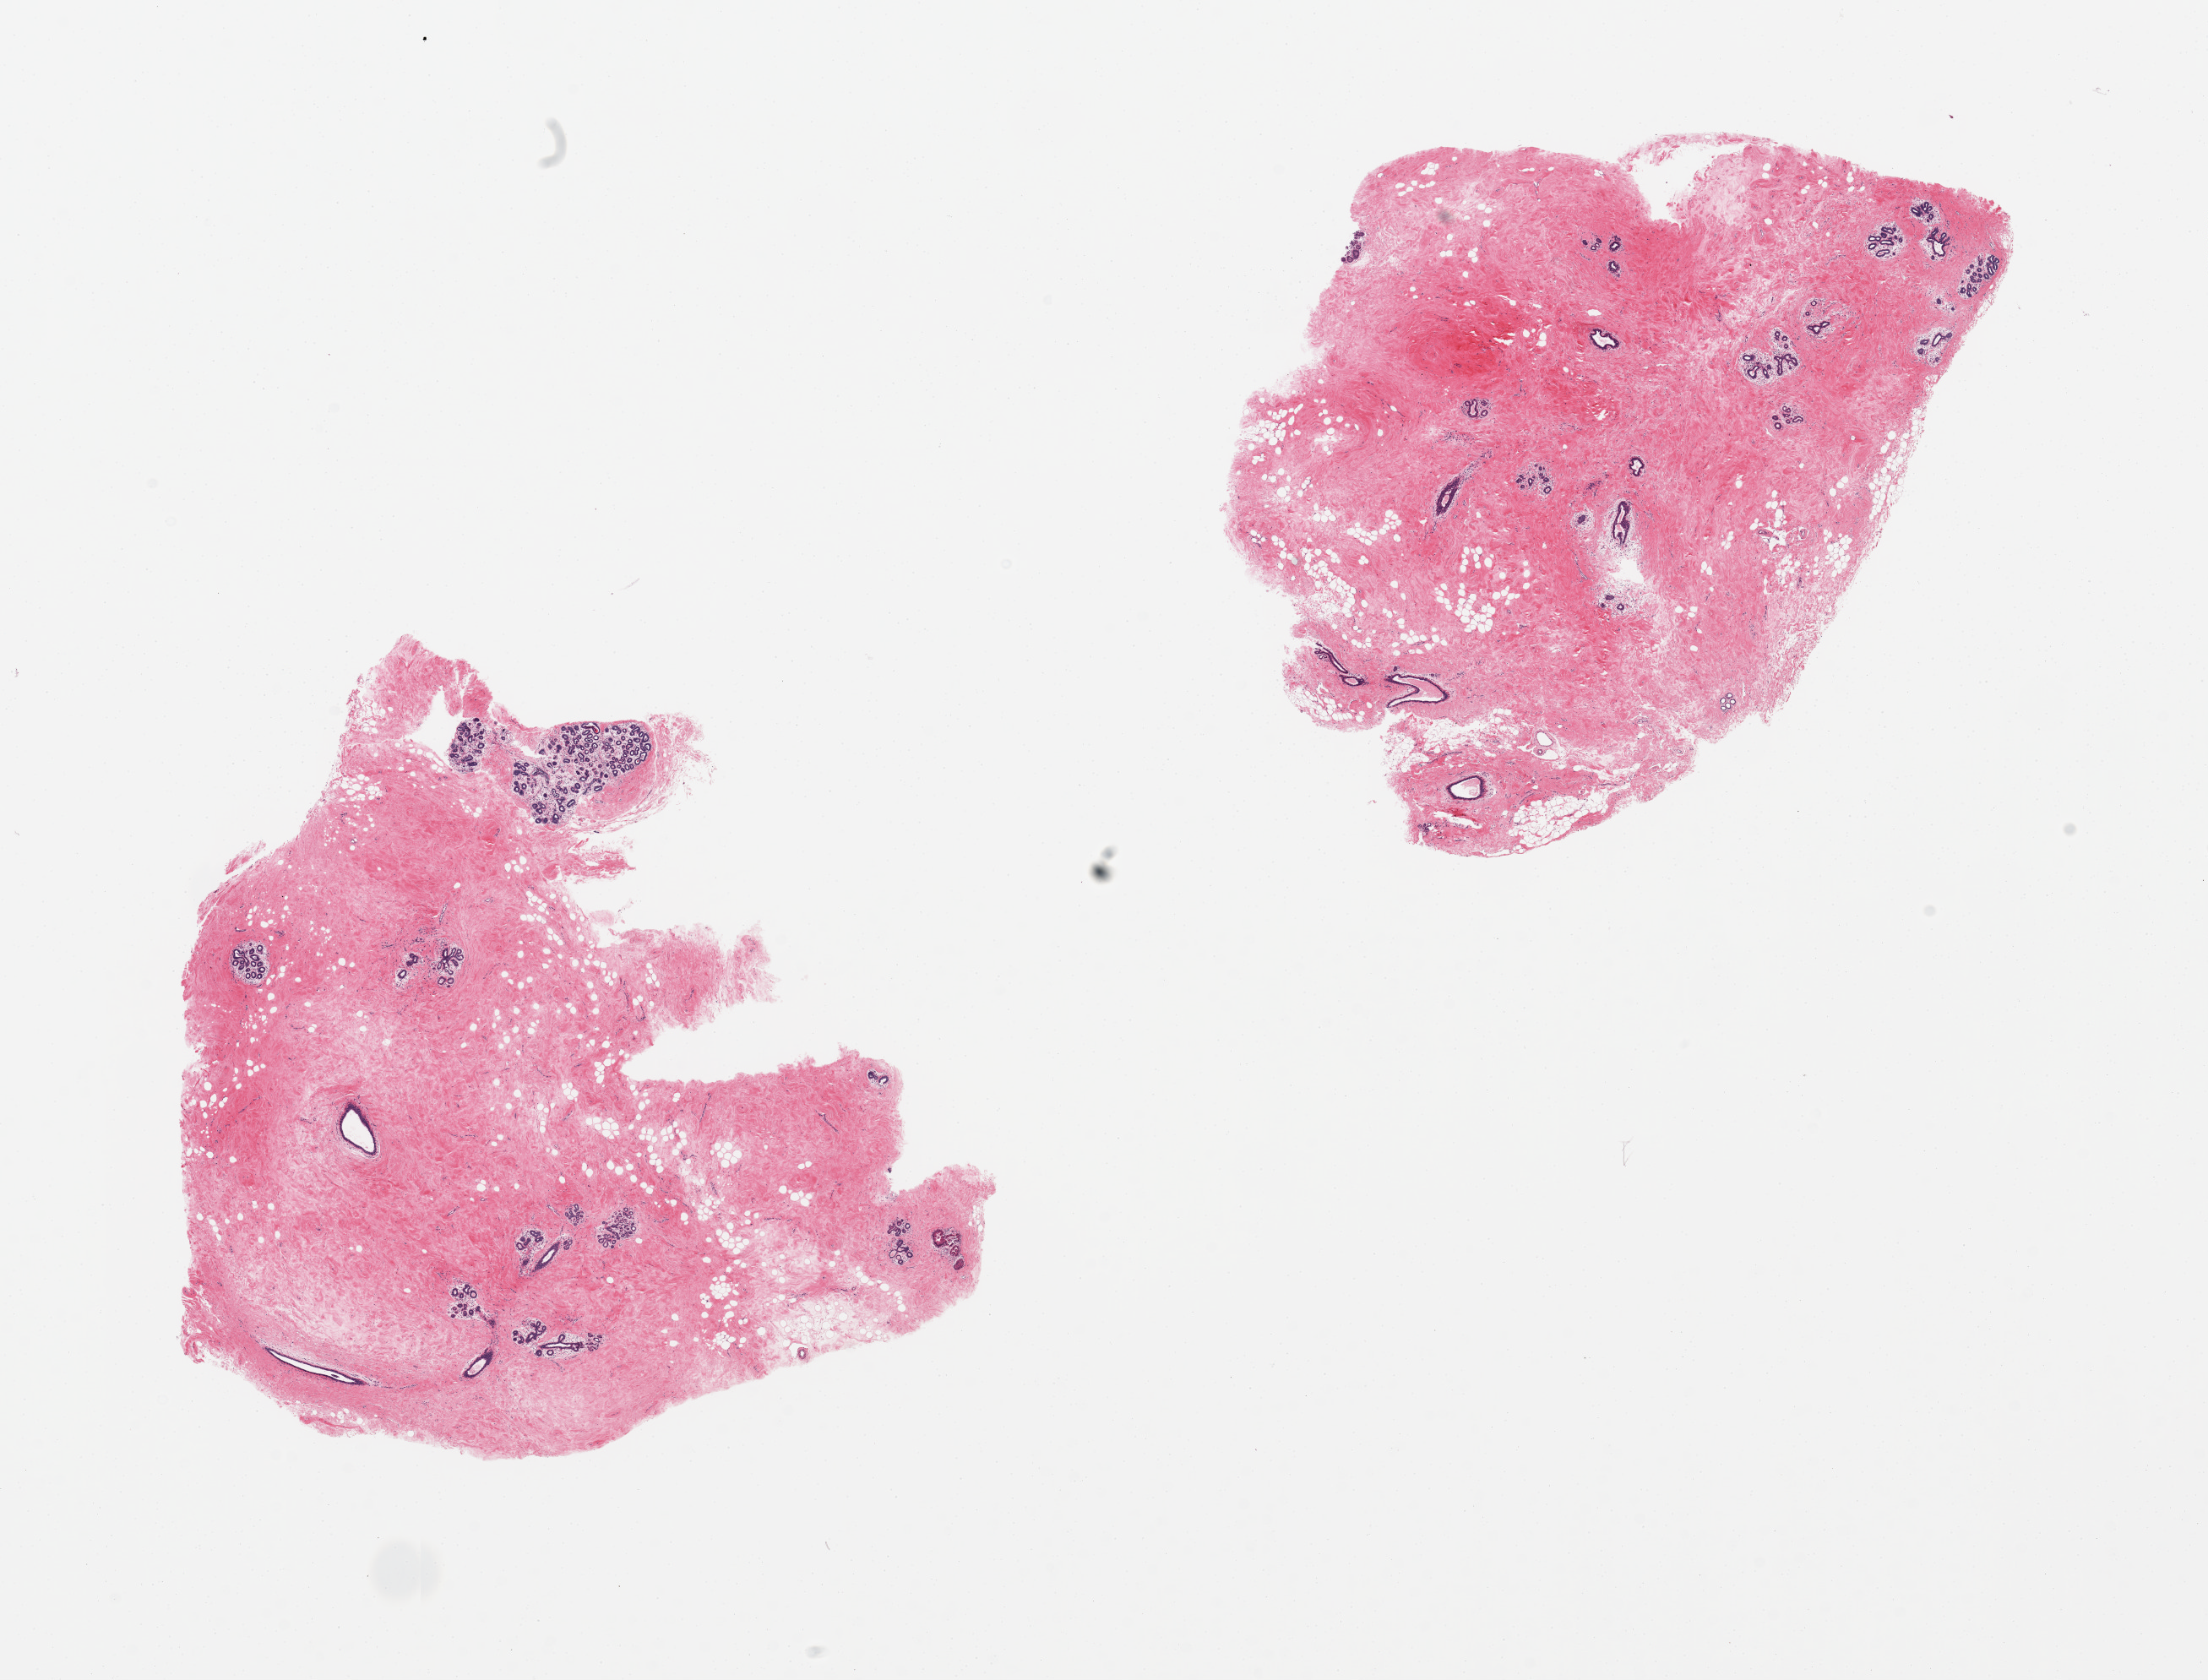
Whole-slide image, hematoxylin and eosin (H&E) stain — a low-resolution overview of the entire scanned area, about 20.7 x 15.7 mm (from a 20x scan), PAXgene-fixed paraffin-embedded (PFPE) section, sampled site (target tissue): breast, tissue donor sample. Female donor.
Pathologist's review note for this sample: 2 pieces, predominantly fibrous stroma with good representation of ducts and lobules (~10%), some apocrine change.